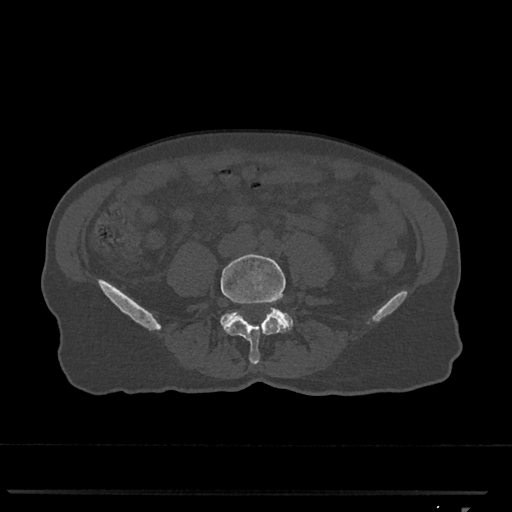
CT including the spine, one axial slice; position 191 of 793 along the scan axis; bone window (W 1800 / L 400 HU); 0.5 mm slice thickness; 512 × 512 image matrix. Patient: female, 62 years. Case-level facts recorded for this patient, not image findings: primary cancer: renal.
Structures marked on this image (semi-automatically segmented with operator editing):
- L4 vertebra: bounding box <221,254,288,365> (left, top, right, bottom; pixels)
- L5 vertebra: <220,309,293,330>